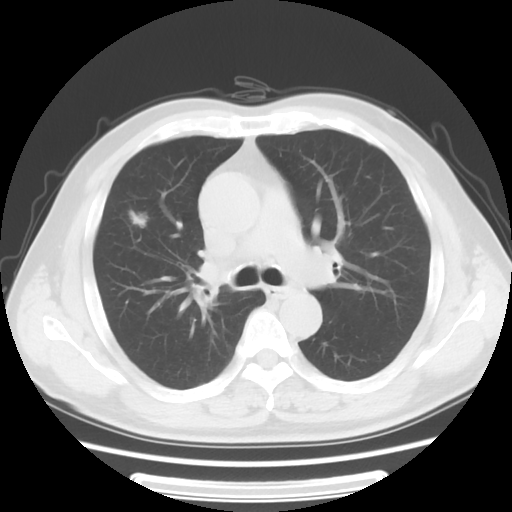
Chest CT, one axial slice; slice 38 of 63 in the series (ordered by position); lung window (W 1500 / L -600 HU); 512 × 512 image matrix, field of view 360 × 360 mm. Patient: male, 63 years. From the clinical record (not read from this slice): clinical TNM (as recorded): T1c N0 M0; histopathological grade: G2-3.
Structures marked on this image (rectangle marked by the reading radiologist):
- lung tumour (recorded histology: adenocarcinoma): bounding box (x1, y1, x2, y2) in pixels: (118, 200, 151, 240)